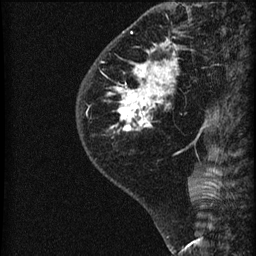
Breast MRI (dynamic contrast-enhanced), one sagittal slice; slice 20 of 60 in the series (ordered by position); dynamic contrast-enhanced series, image 2 of 3 at this slice position (ordered by acquisition); 1.5 T; TE 4.2 ms, TR 22.7 ms; 1.8 mm slice thickness; 256 × 256 image matrix. Female patient, age 45 years. Case-level facts recorded for this patient, not image findings: setting: breast cancer imaged before/during neoadjuvant chemotherapy; receptor status: HR-positive, HER2-negative.
Outlined on this slice (semi-automatic segmentation, software-assisted and operator-edited):
- analysis volume of interest (the breast-tissue region the enhancement analysis was run in; not a lesion): bounding box <77,11,205,140> (left, top, right, bottom; pixels)
- tumour enhancement mask (voxels above the 90 % enhancement threshold inside the analysis volume of interest): <114,41,178,131>